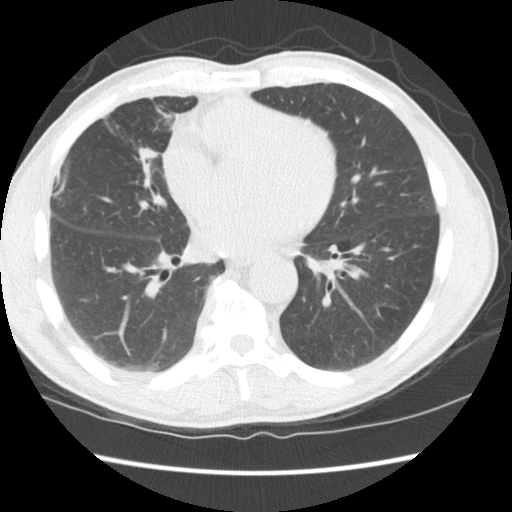
Low-dose screening chest CT, axial slice, third screening round (two years after baseline), lung window (W 1500 / L -600 HU), 2.5 mm slice thickness, standard (soft-tissue) reconstruction kernel (STANDARD). Male, age 65 years at enrolment. Current smoker at enrolment.
Expert reader's lesion annotation, bounding box (x1, y1, x2, y2) in pixels: (108, 133, 170, 207). The exam's reader record, not a measurement of the box and not confirmed to be the same lesion: non-calcified nodule or mass ≥4 mm, right middle lobe, 16 × 15 mm, smooth margins, soft tissue attenuation, pre-existing on the prior screen: yes; interval growth: yes. Later outcome: lung cancer diagnosed 357 days after this screen — squamous cell carcinoma, NOS, right middle lobe, poorly differentiated (G3), stage IA (AJCC 6th edition), 23 mm at pathology.